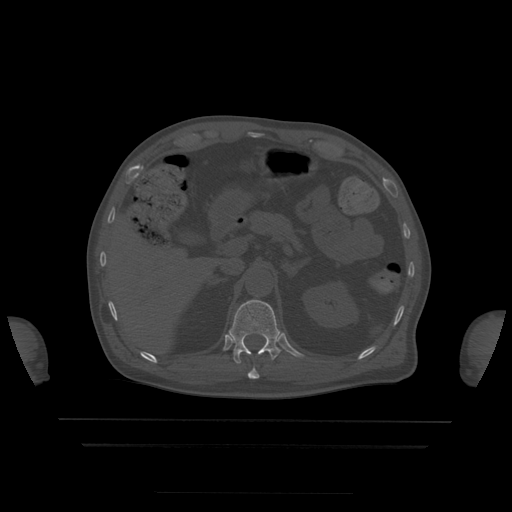
CT including the spine, one axial slice. Position 201 of 522 along the scan axis. Bone window (W 1800 / L 400 HU). 1.25 mm slice thickness. 512 × 512 image matrix. Patient age 68 years. Case-level facts recorded for this patient, not image findings: primary cancer: urothelial.
Annotated regions visible in this slice (semi-automatically segmented with operator editing):
- T11 vertebra: bounding box <248,368,260,379> (left, top, right, bottom; pixels)
- T12 vertebra: <229,299,281,364>